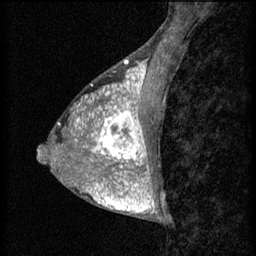
Breast MRI (dynamic contrast-enhanced), one sagittal slice. Position 24 of 60 along the scan axis. 3 images stored at this slice position (order not interpretable as contrast timing). 1.5 T. TE 4.2 ms, TR 8.2 ms. 256 × 256 image matrix, field of view 180 × 180 mm. Patient: female, 38 years.
Annotated regions visible in this slice (semi-automatically segmented with operator editing):
- analysis volume of interest (the breast-tissue region the enhancement analysis was run in; not a lesion): box from (x=95, y=106) to (x=157, y=171) px
- tumour enhancement mask (voxels above the 70 % enhancement threshold inside the analysis volume of interest): (x=95, y=106)–(x=149, y=171)